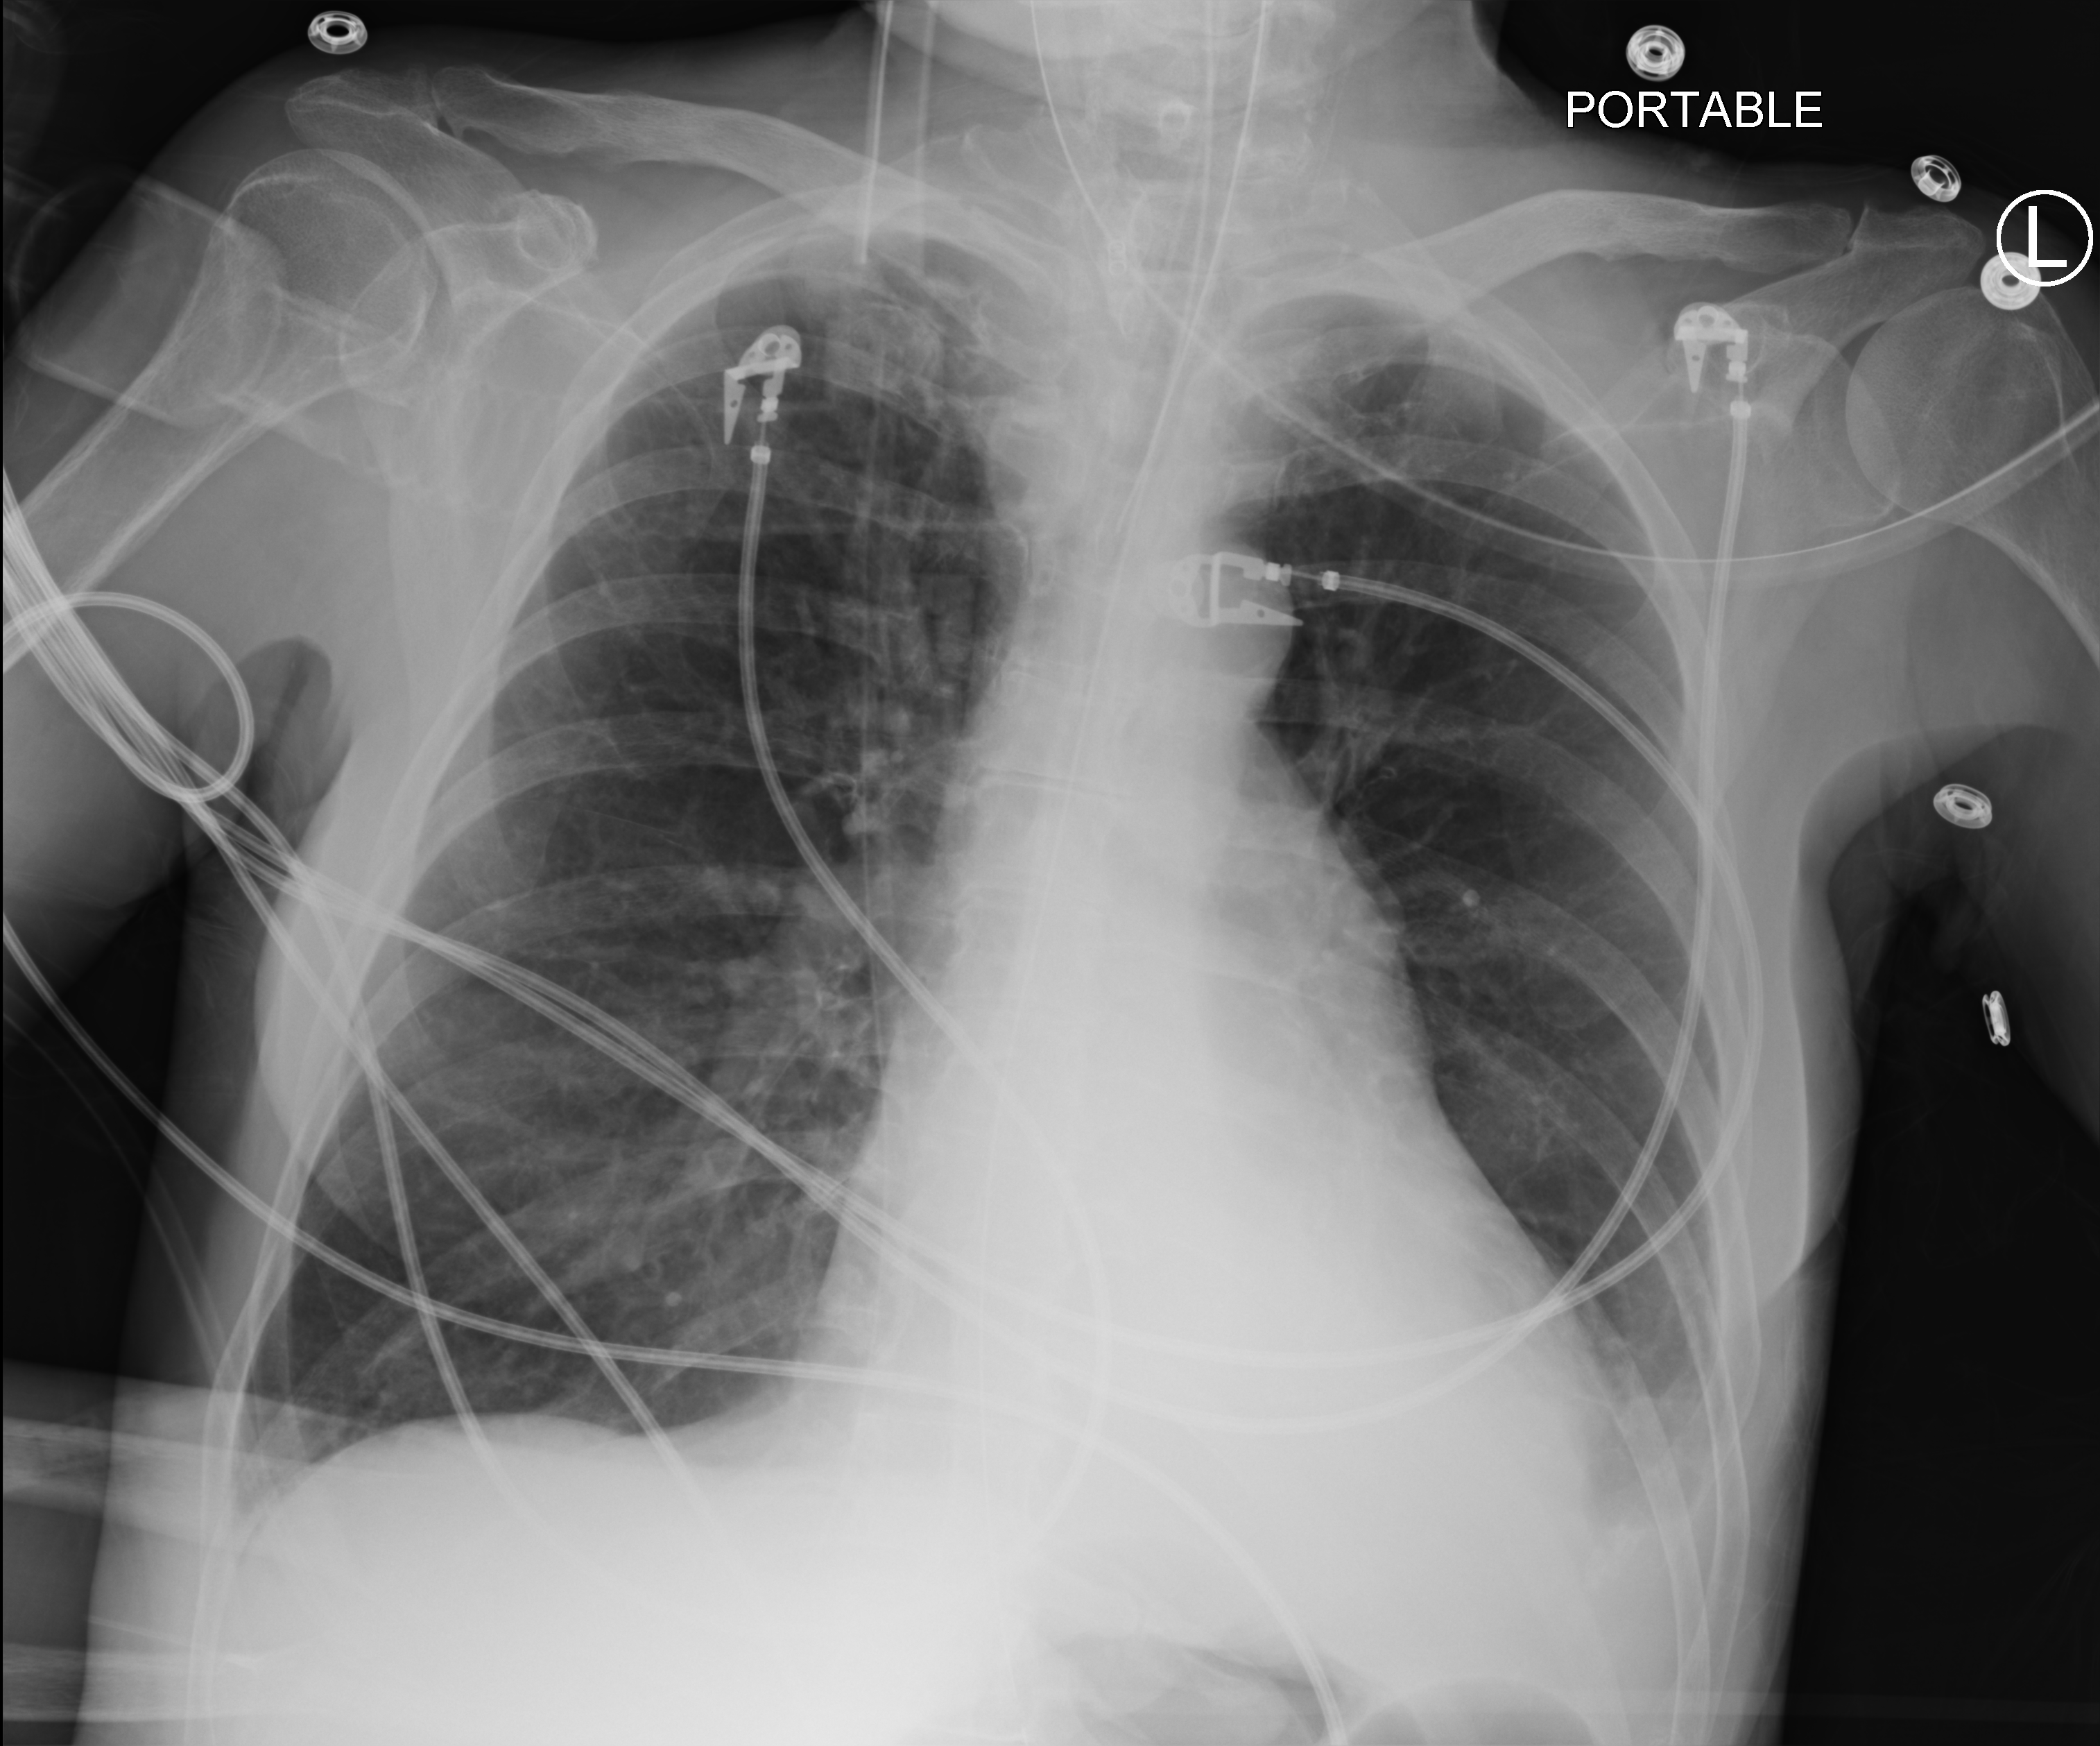
Portable chest radiograph; anteroposterior (AP) projection. Patient hospitalised with COVID-19; female, aged 60–74 years.
From the hospital-stay record, not from the radiograph (when in the stay this image was taken is not recorded):
- admitted to intensive care during this hospital stay: yes
- mechanically ventilated during this hospital stay: yes